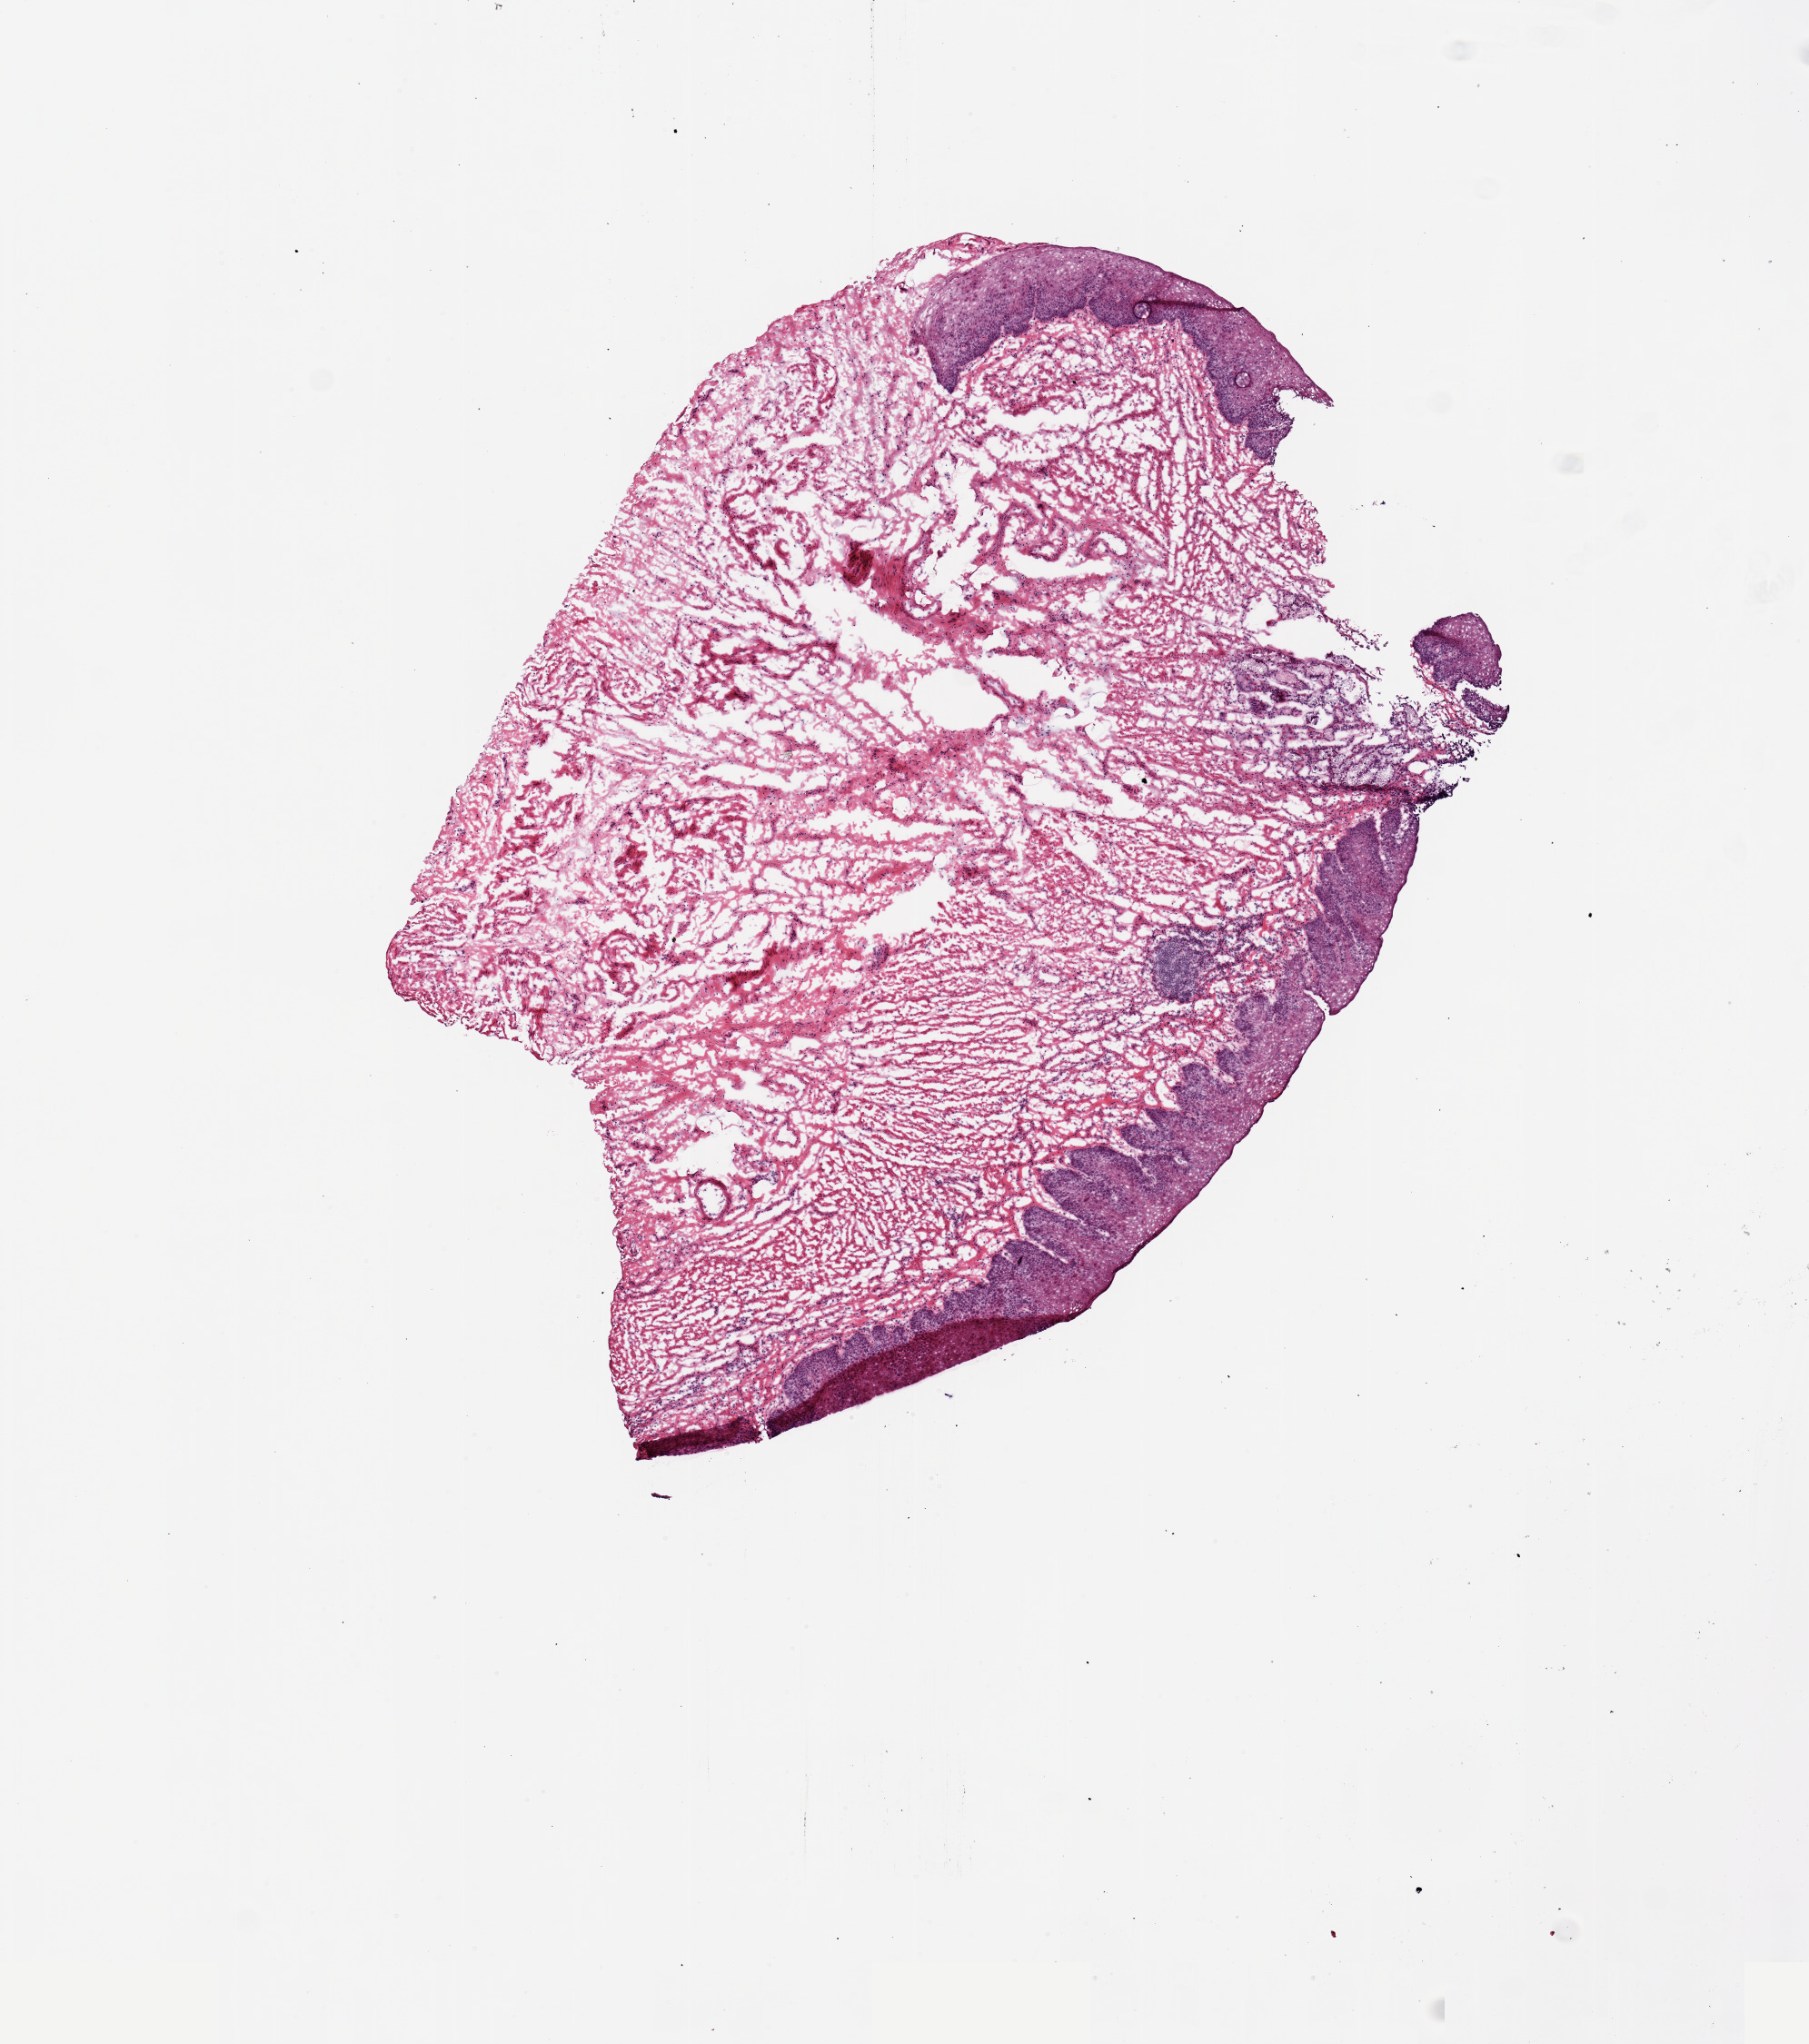
Digitized hematoxylin and eosin (H&E)-stained section, a low-resolution overview of the entire scanned area, about 7.9 x 8.9 mm (from a 20x scan). Frozen section (dry ice). Section of esophageal mucous membrane (target tissue). Tissue donor sample. Donor sex: male.
Pathologist's review note for this sample: 1 piece; squamous epithelium present; unacceptable based on PAXgene unacceptability.